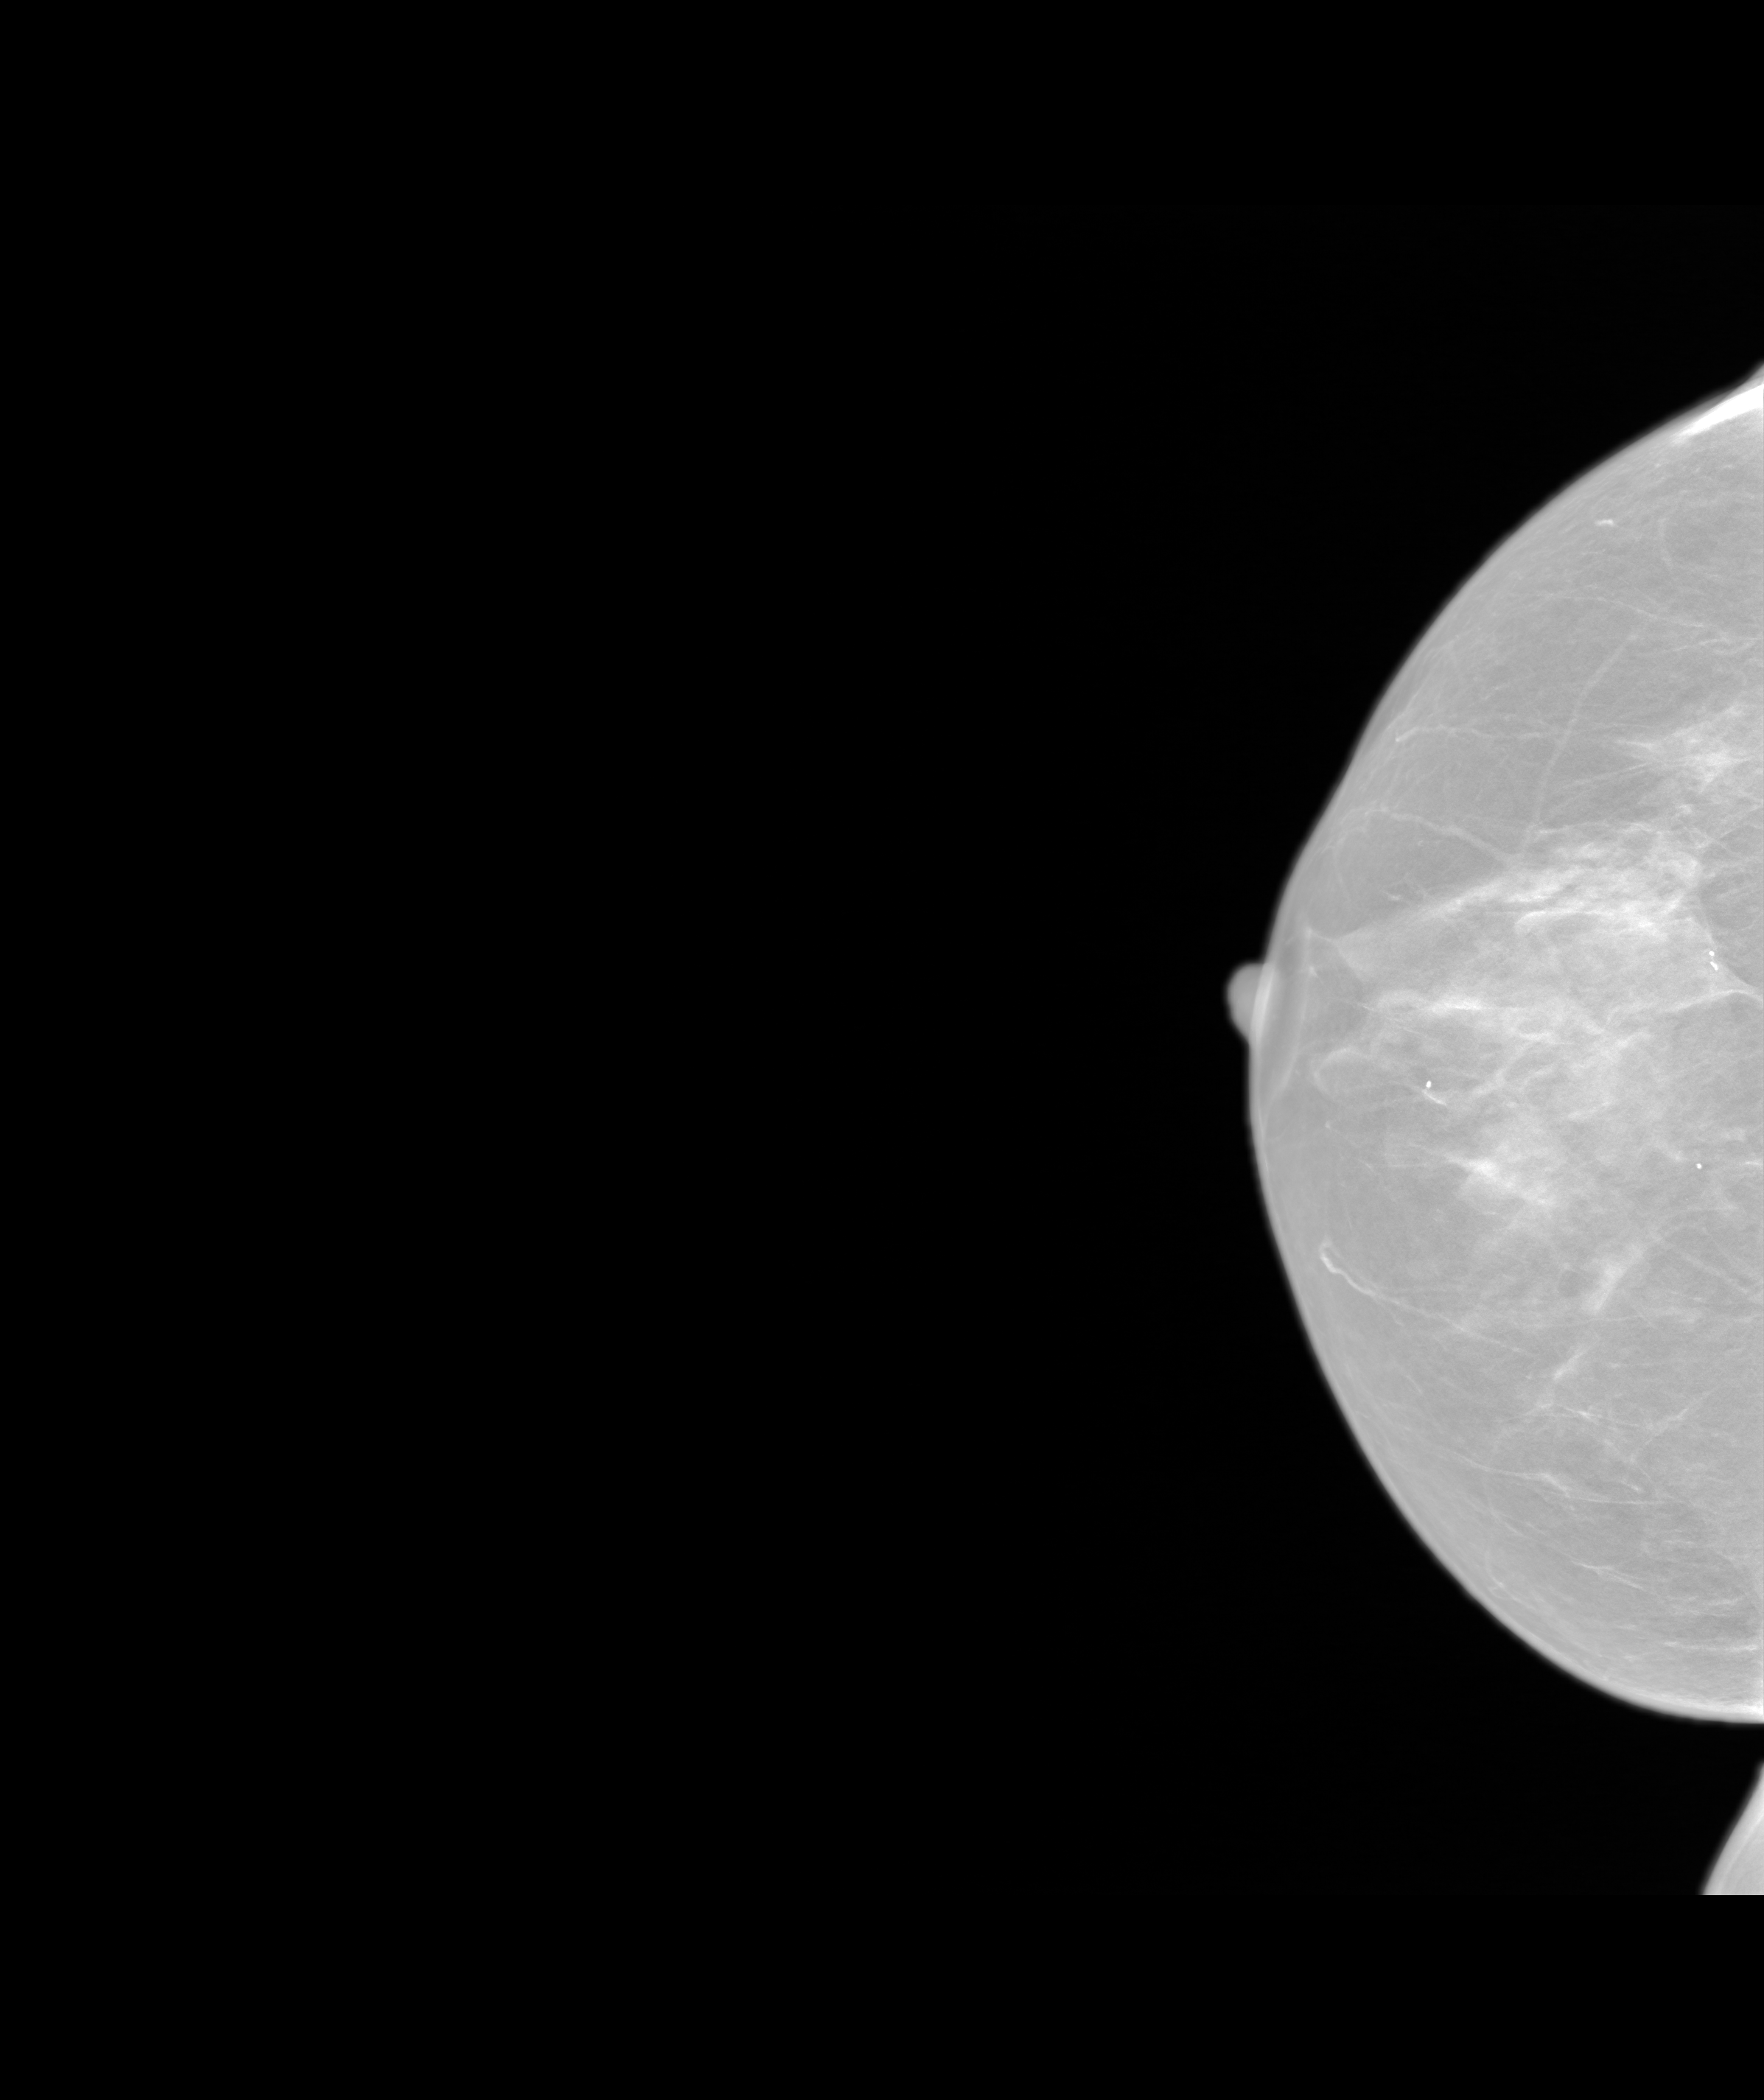
Screening examination.
Image type: synthesized 2-D view from tomosynthesis. Breast: right. Projection: CC view.